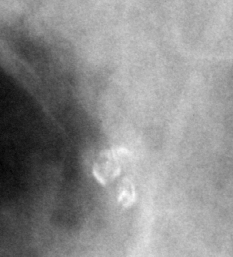
Region of interest cut from a scanned film mammogram (one marked finding); right breast; MLO view; BI-RADS breast density category 3 (scale 1–4).
- Marked abnormality: calcifications, morphology lucent center; BI-RADS assessment category 2; benign without callback (not worked up further).